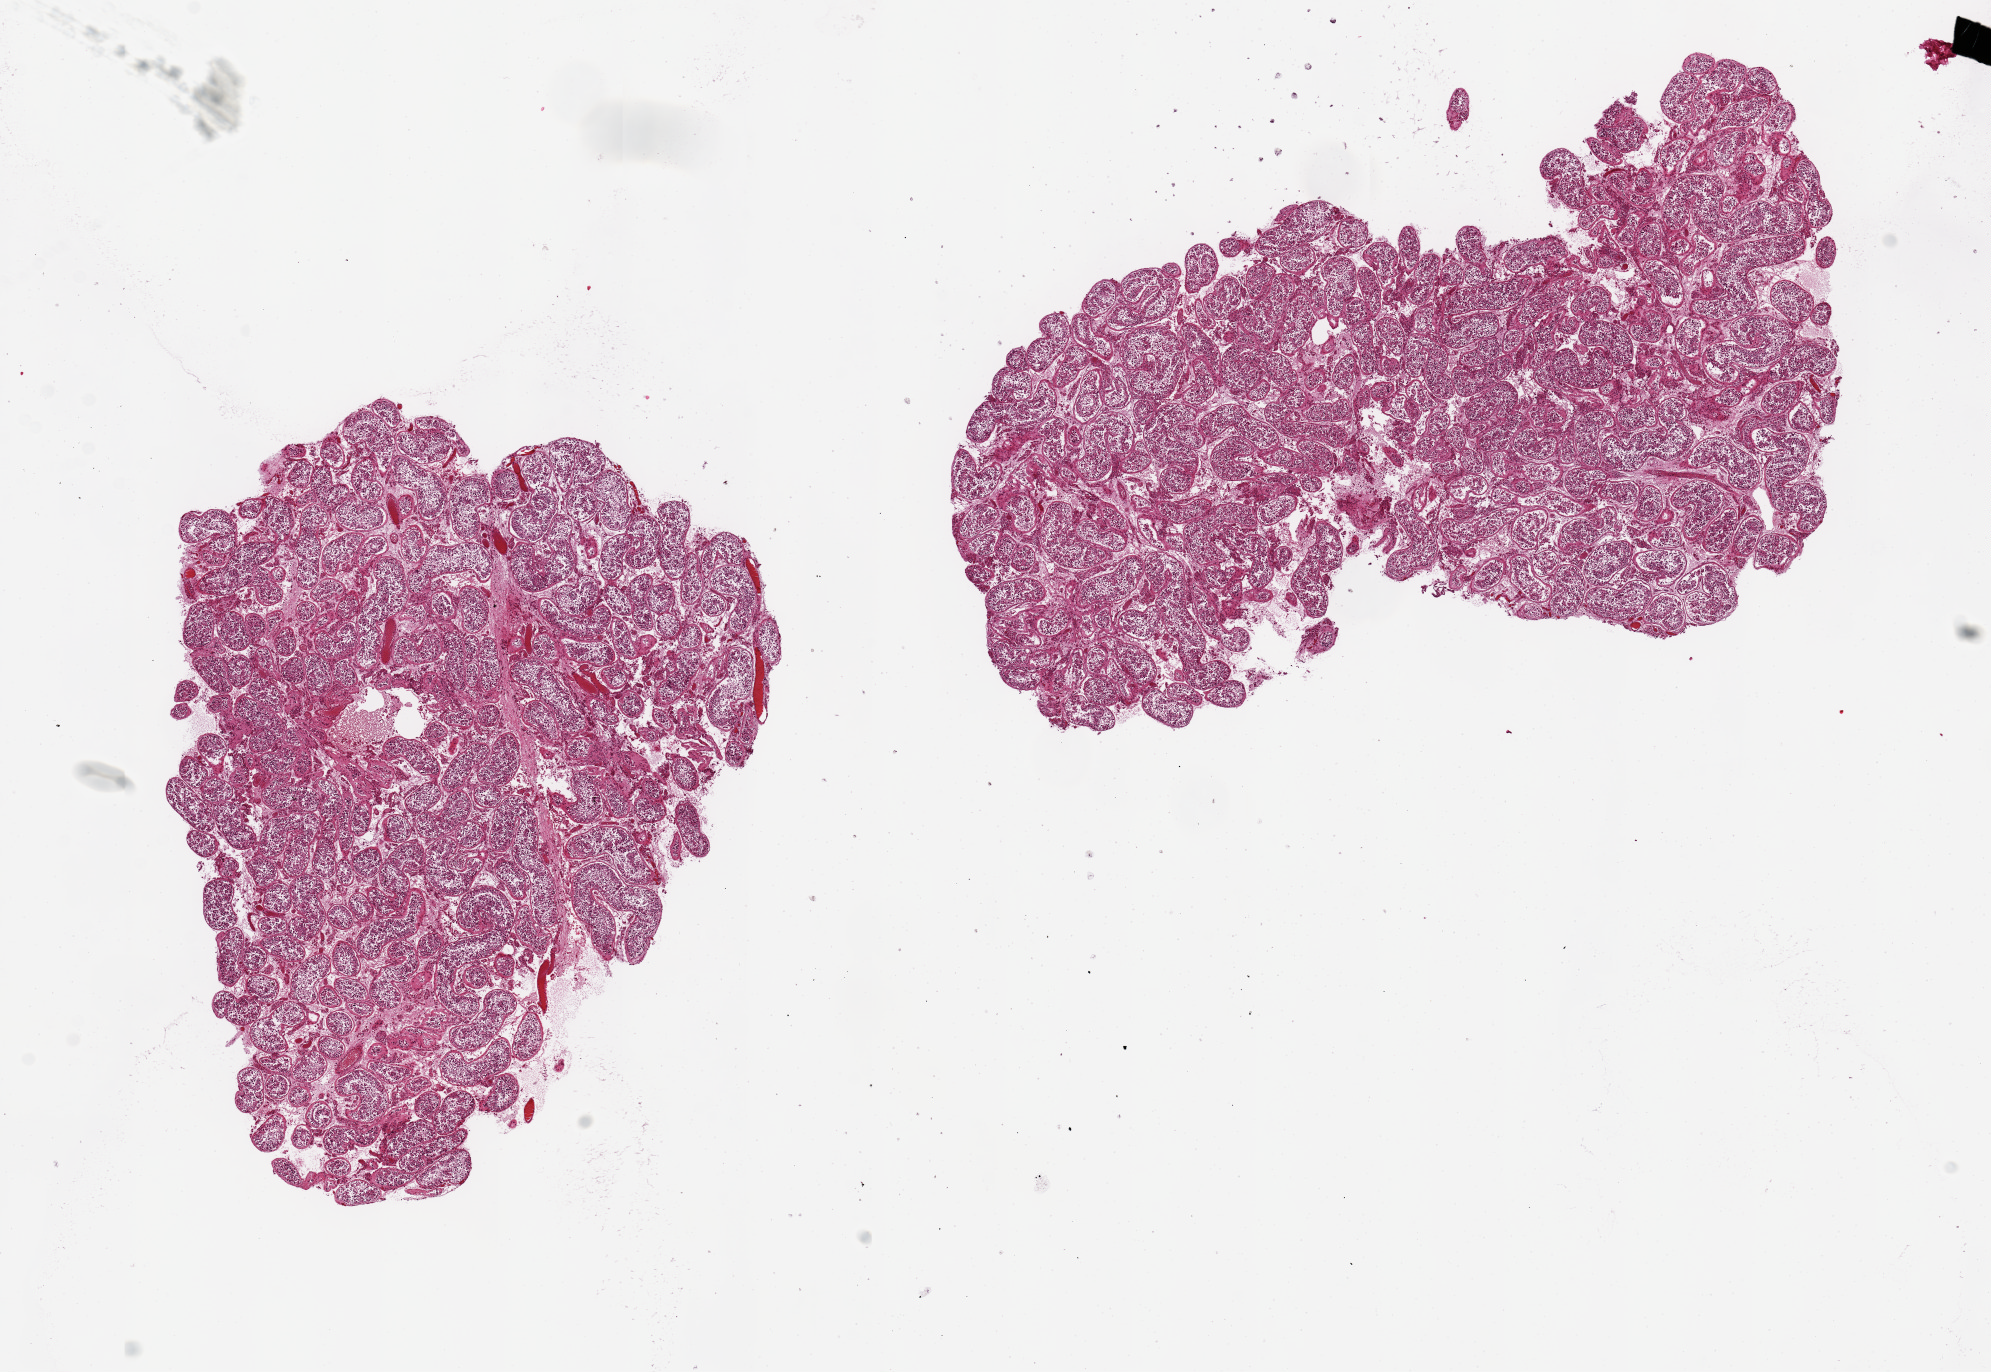
Whole-slide image, haematoxylin and eosin stain, shown as a low-resolution overview of the whole scanned area (about 15.8 x 10.9 mm, from a 20x scan); PAXgene-fixed, paraffin-embedded tissue; section of testis (target tissue); donor tissue sample. Male donor.
Review note (as recorded): 2 pieces, 6x5 & 7x4.5mm; spermatogenesis is present; badly autolyzed.